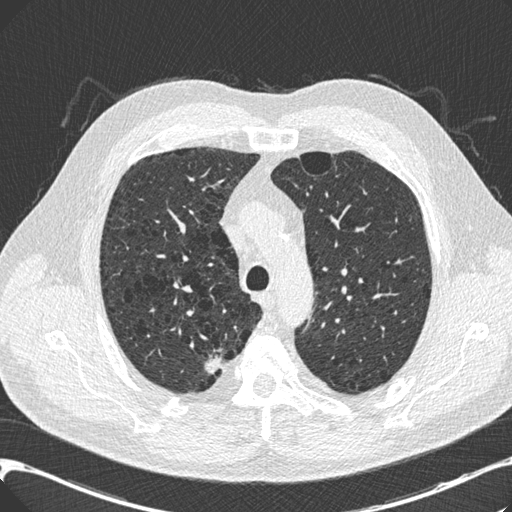
Chest CT (low-dose screening protocol), one axial image, third screening round (two years after baseline), lung window (W 1500 / L -600 HU), standard (soft-tissue) reconstruction kernel (B30f), 120 kVp, slice 49 of 197 in the series, 512 × 512 image matrix. Male participant, aged 68 years at enrolment. Current smoker at enrolment.
Expert reader's lesion annotation, bounding box [x1, y1, x2, y2] px = [189, 347, 235, 387]. The screening reader recorded 3 non-calcified nodules or masses ≥4 mm on this exam (right upper lobe, right upper lobe, left lower lobe); which of them this box marks is not recorded. Official screen result: positive, other. Lung cancer was diagnosed 46 days after this screen: adenocarcinoma, NOS, right upper lobe, well differentiated (G1), stage IB (AJCC 6th edition), 15 mm at pathology.